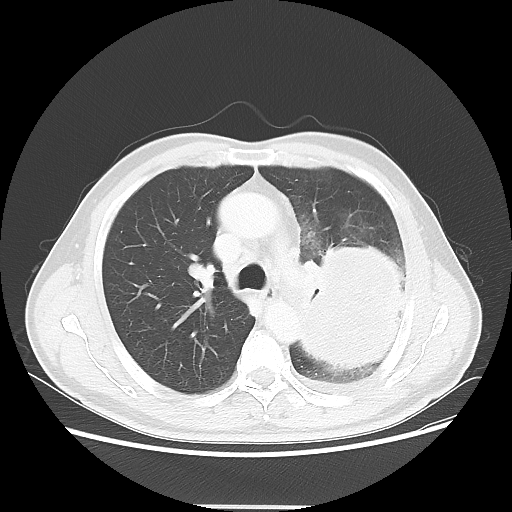
Chest CT, one axial slice; position 36 of 53 along the scan axis; reconstruction kernel LUNG; lung window (W 1500 / L -600 HU); 5 mm slice thickness; 512 × 512 image matrix, field of view 391 × 391 mm. Patient: male, 60 years. Case-level facts recorded for this patient, not image findings: clinical TNM (as recorded): T4 N1 M1a; histopathological grade: G3.
Outlined on this slice (bounding box drawn by a radiologist):
- lung tumour (recorded histology: large cell carcinoma): bounding box <291,224,411,385> (left, top, right, bottom; pixels)